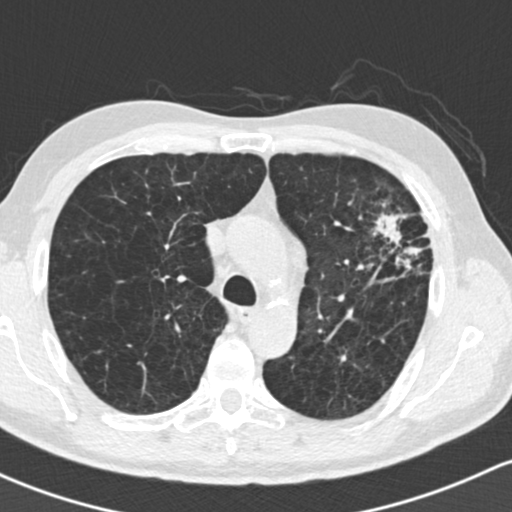
Chest CT (low-dose screening protocol), one axial image, baseline screening round, lung window (W 1500 / L -600 HU), 2 mm slice thickness, slice 53 of 162 in the series, 512 × 512 image matrix, field of view 318 × 318 mm. Male participant, aged 61 years at enrolment. Former smoker at enrolment.
Expert reader's lesion annotation, bounding box <353,184,446,289> (left, top, right, bottom; pixels). Reader record for this screening exam (exam-level; its link to the box is not recorded): non-calcified nodule or mass ≥4 mm, left upper lobe, 35 × 35 mm, spiculated (stellate) margins, soft tissue attenuation. Participant outcome: lung cancer diagnosed 19 days after this screen — adenocarcinoma, NOS, left upper lobe, well differentiated (G1), stage IIIA (AJCC 6th edition), 45 mm at pathology.